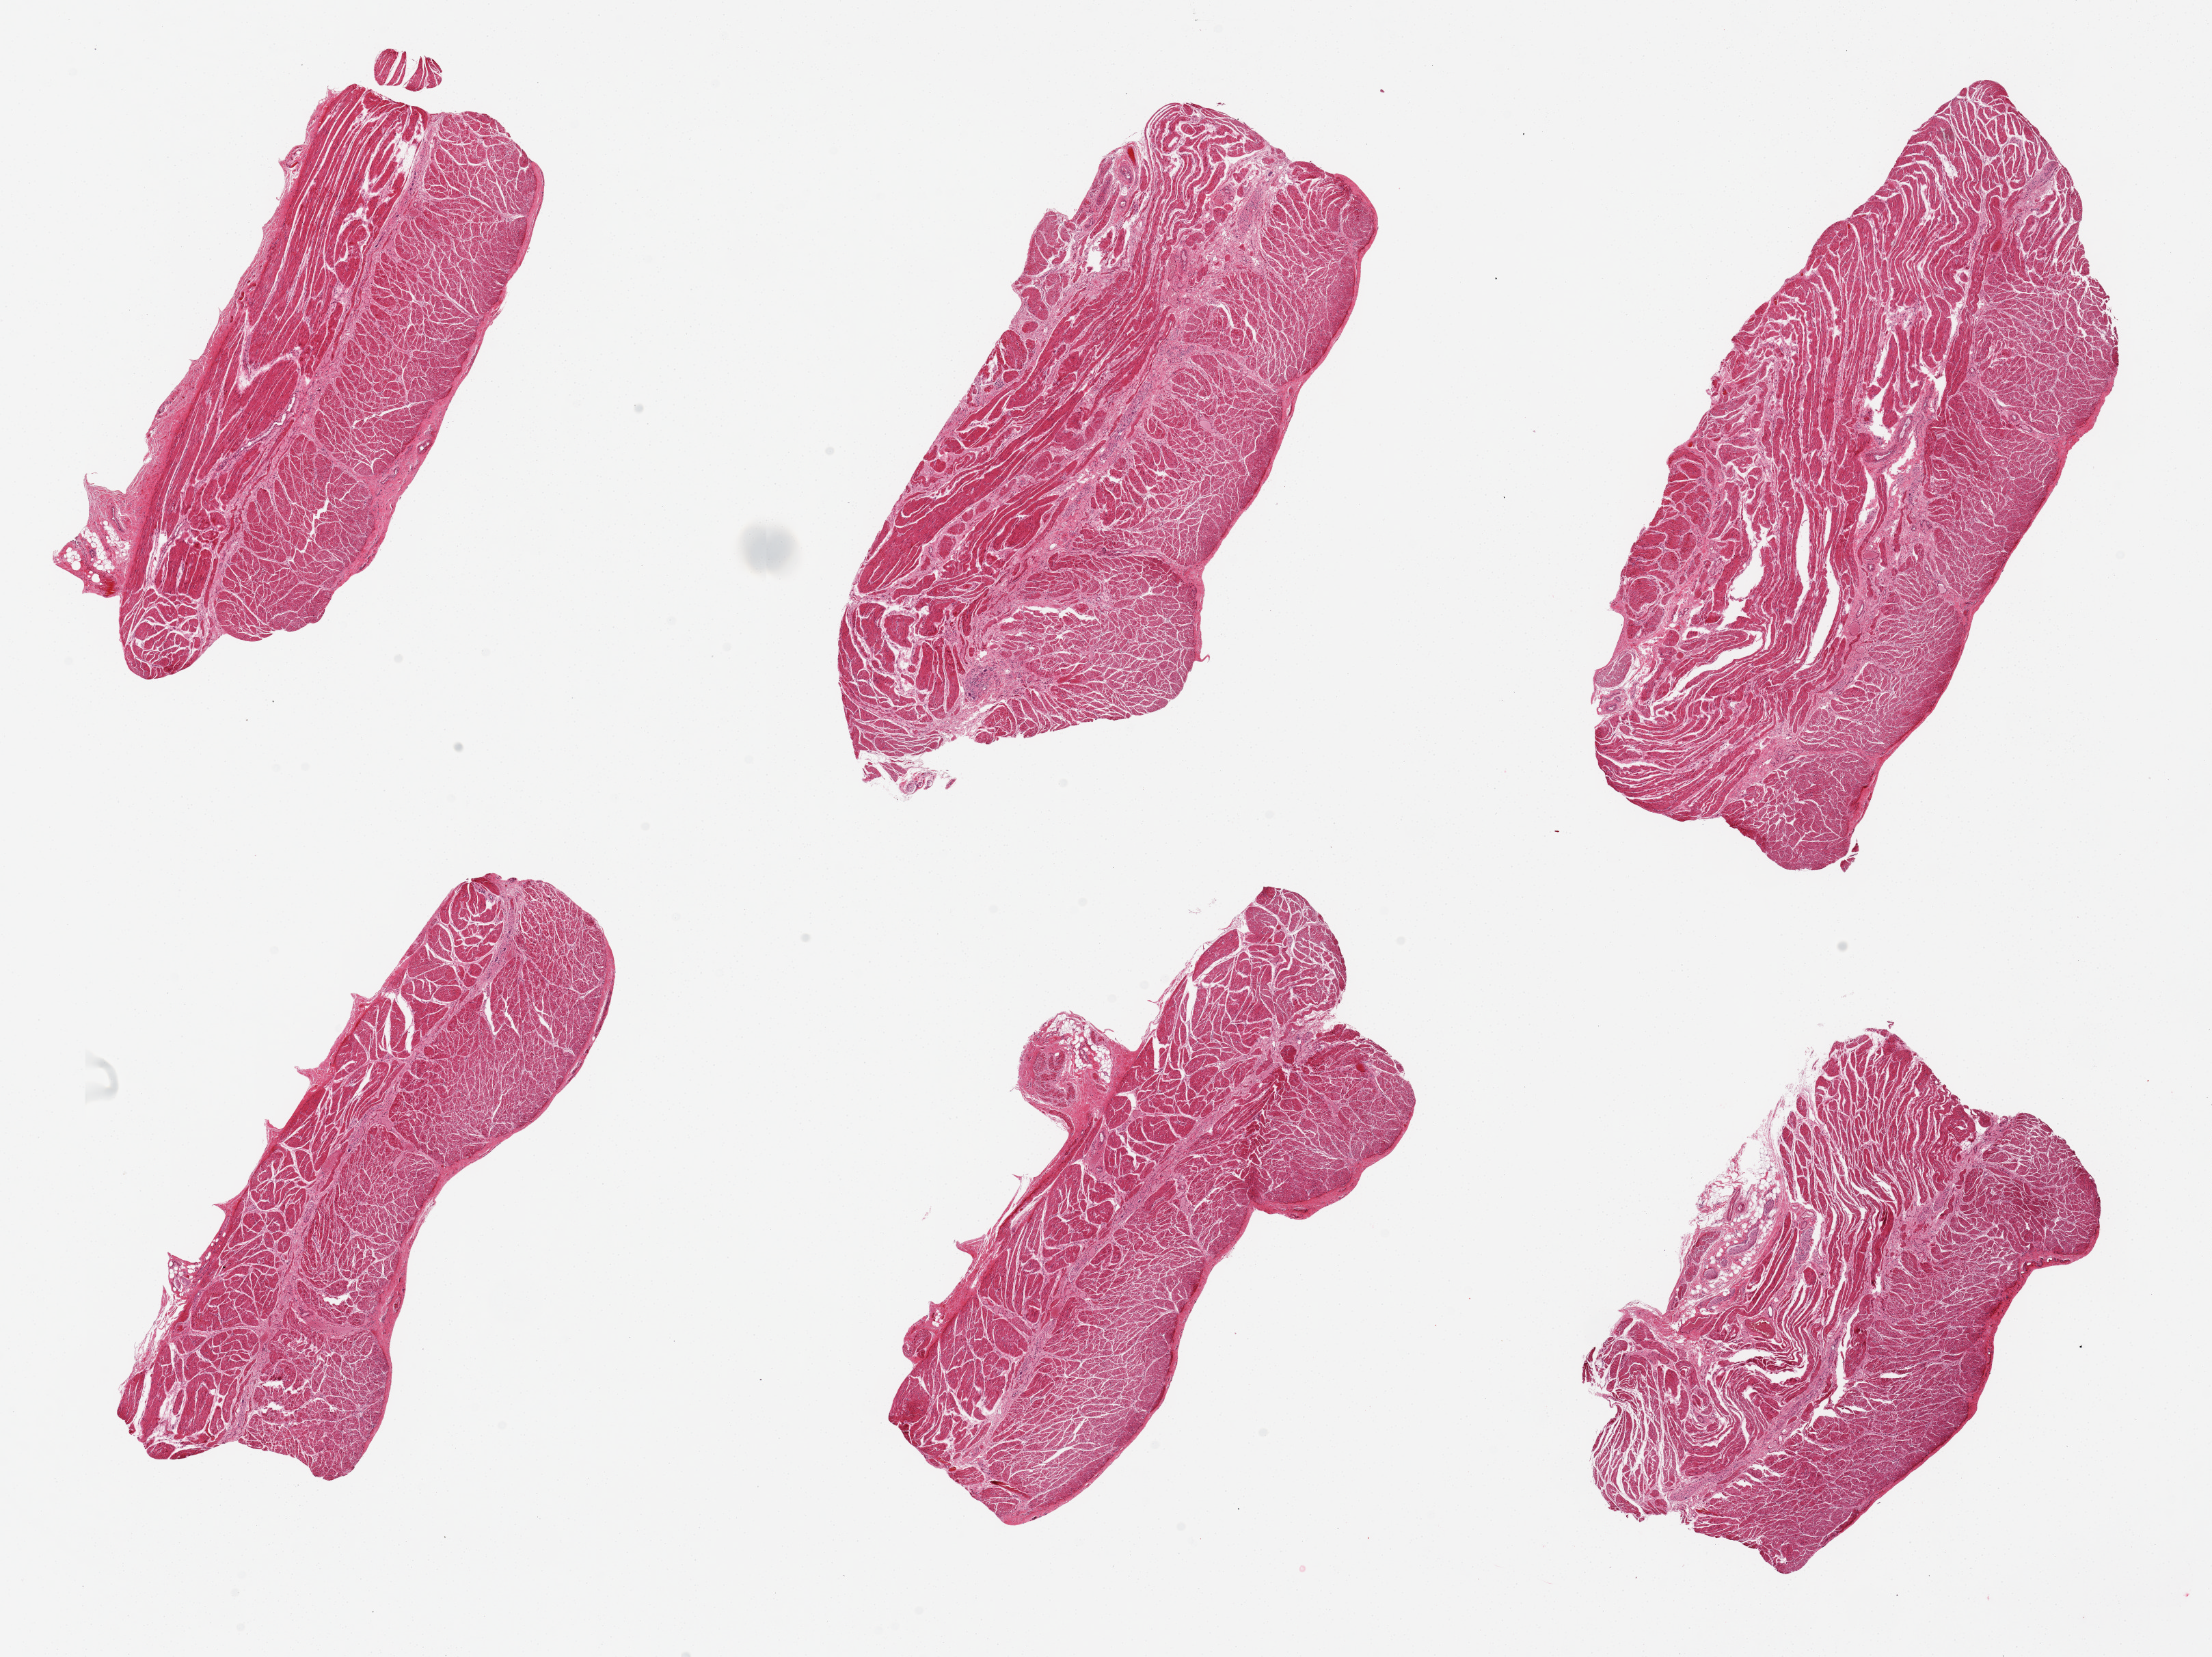
Digitized H&E-stained section, a low-resolution overview of the entire scanned area, about 25.6 x 19.2 mm; PAXgene-fixed, paraffin-embedded tissue; target tissue: esophageal muscle; tissue donor sample. Donor: male.
Review note (as recorded): 6 pieces, from 6x3 to 9x4mm; all muscularis, good specimens.